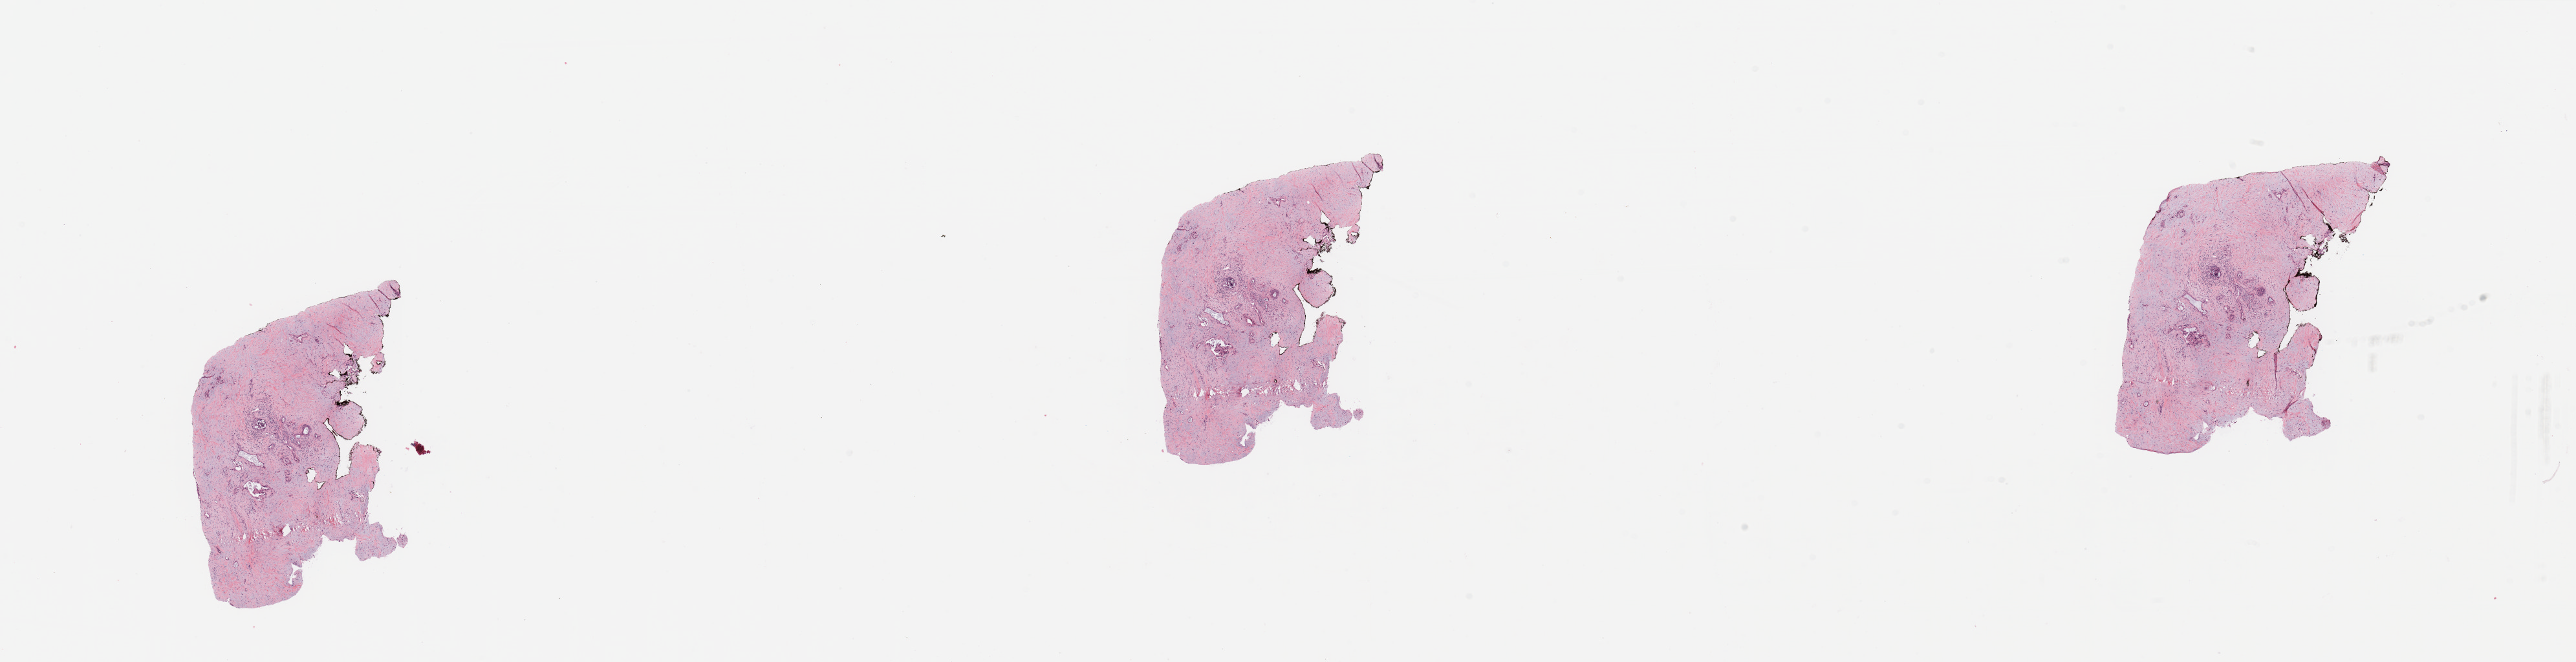
Digitized Hematoxylin and eosin (H&E) stained tissue section (whole slide) — low-resolution overview of the scanned area, about 31.5 x 8.1 mm; tumour tissue sample, sampled site: pancreas. Female, 79 y/o. Composition of this section per pathologist review: tumour nuclei 20%, necrosis 0%.
Diagnosis: Infiltrating duct carcinoma, NOS.